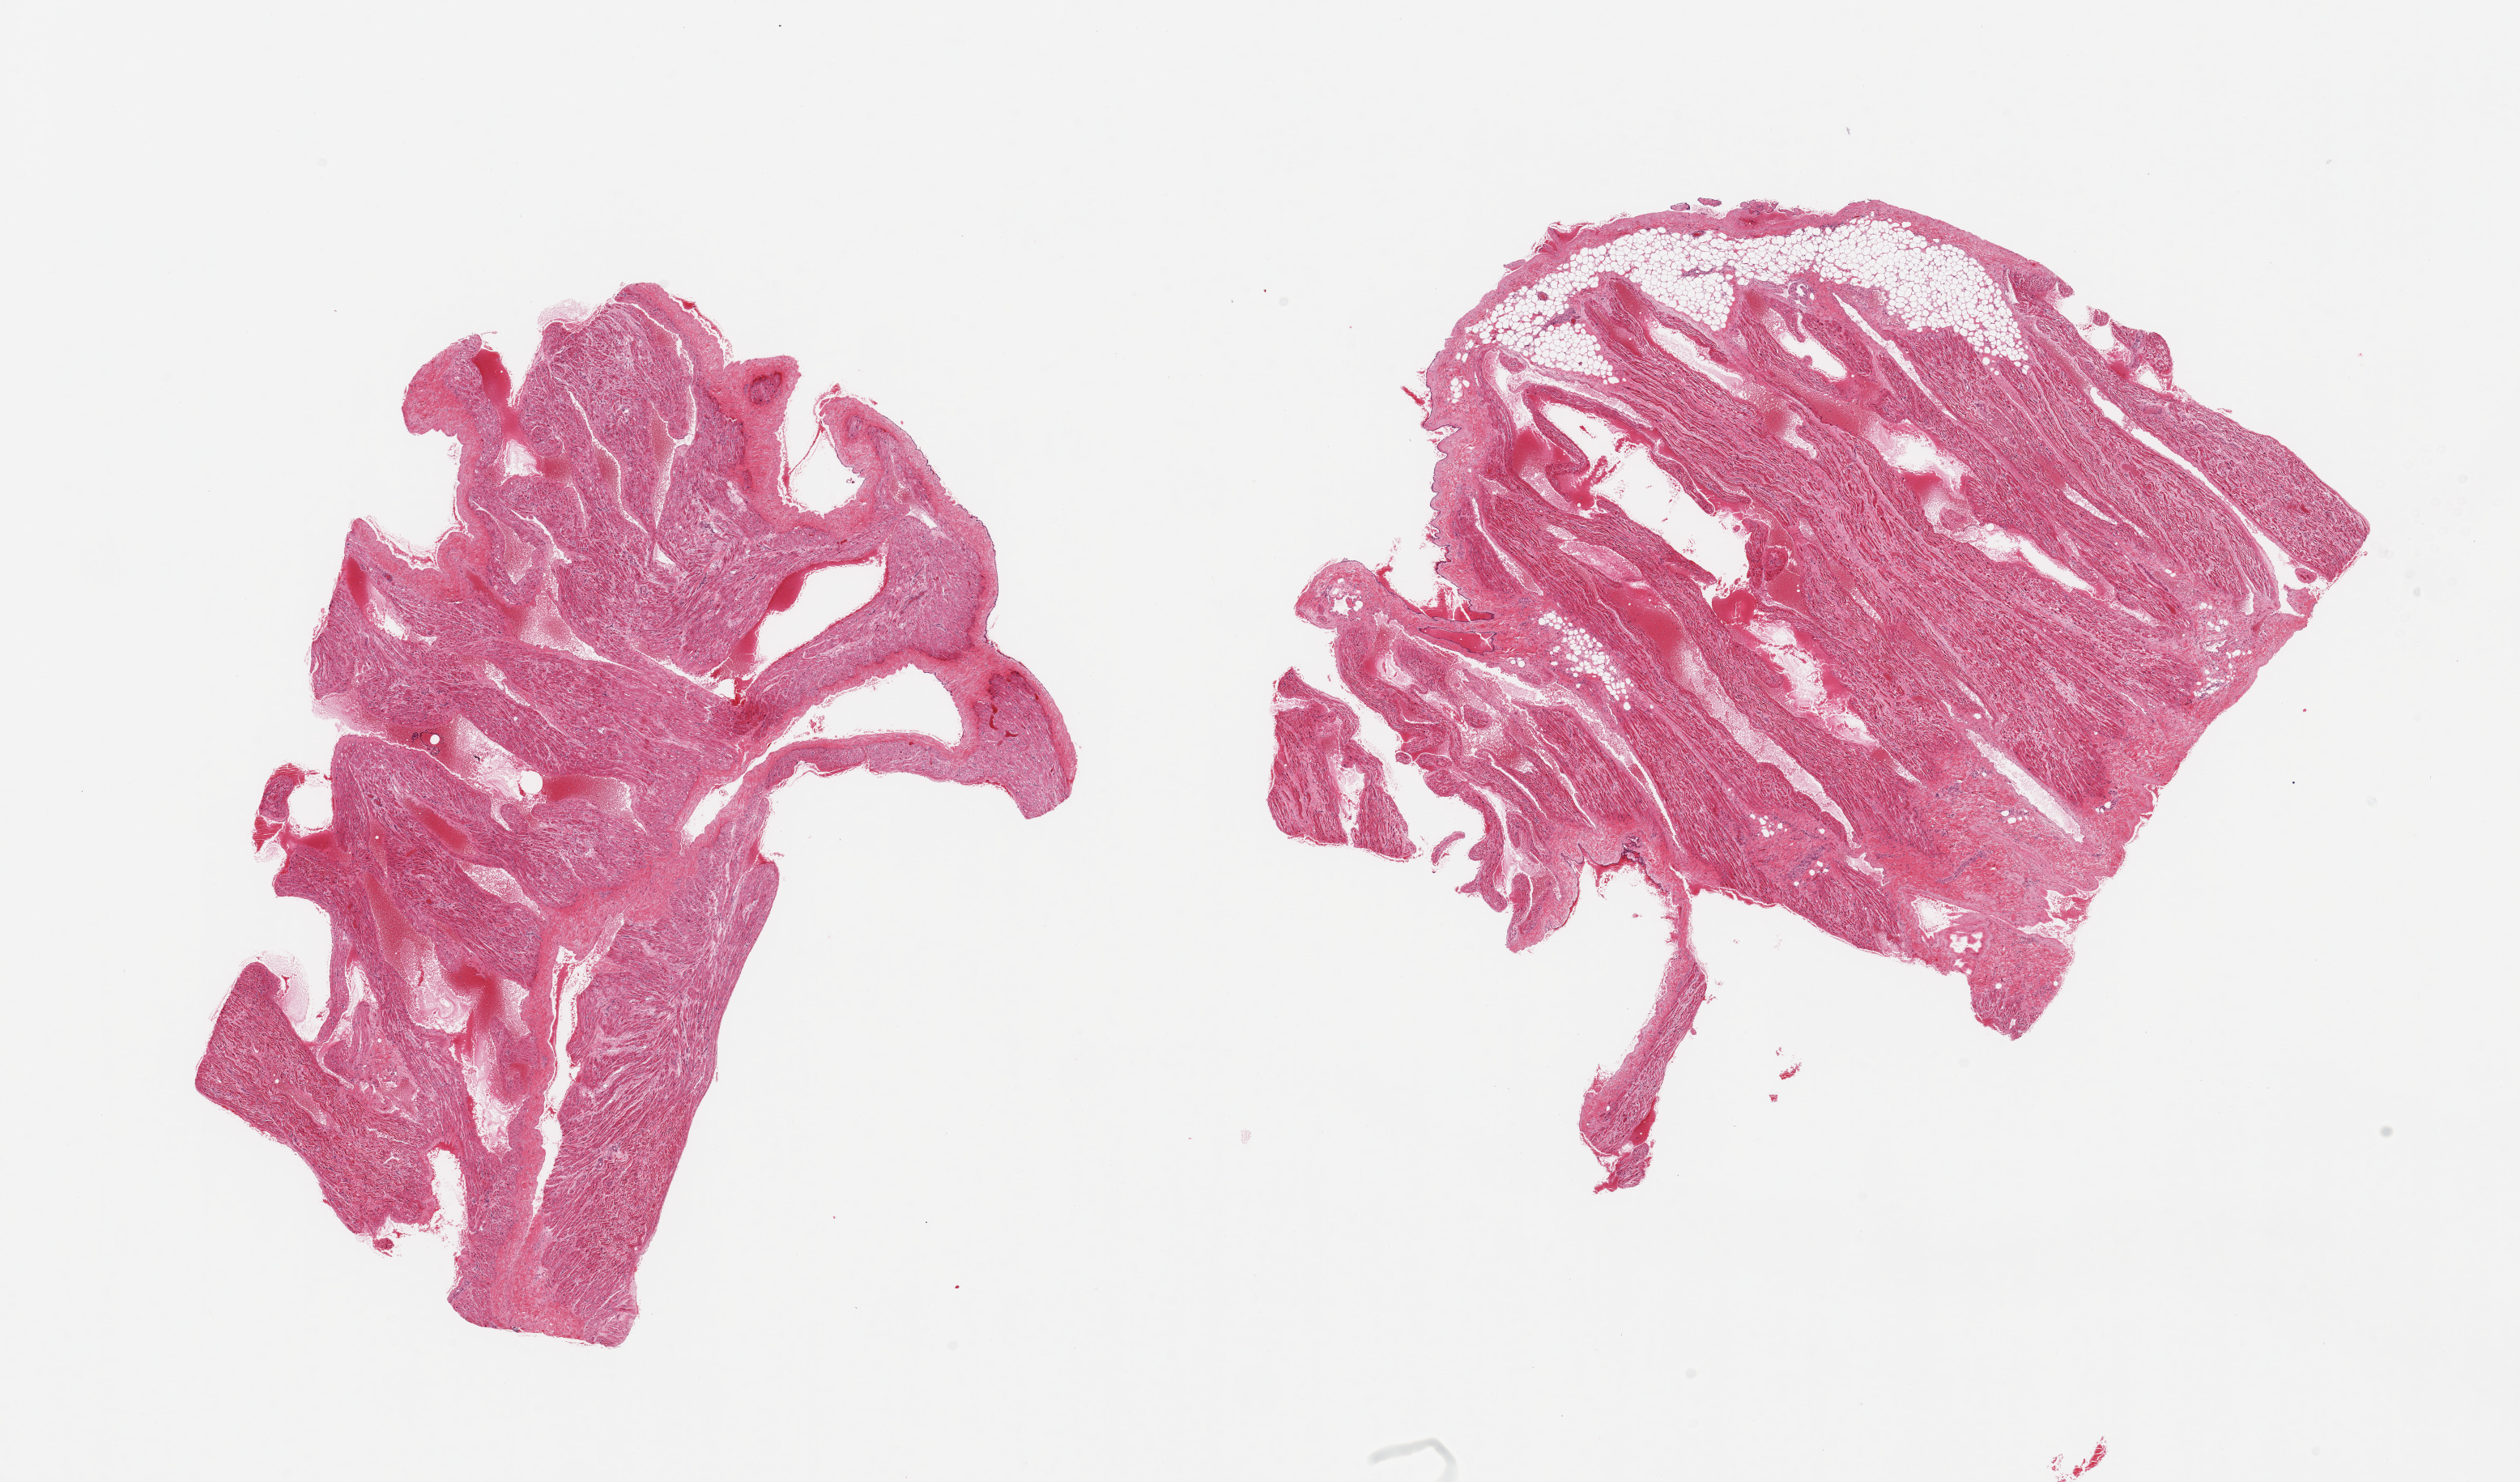
Digitized hematoxylin and eosin (H&E)-stained section — shown as a low-resolution overview of the whole scanned area (about 24.6 x 14.5 mm, slide scanned at 20x), PAXgene-fixed, paraffin-embedded tissue, target tissue: auricular appendage, tissue donor sample. Donor: male.
* reviewer comment on this tissue sample: 2 pieces; 10% external fat on 1 piece